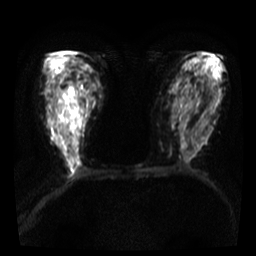
Breast MRI, one axial slice; position 19 of 36 along the scan axis; diffusion-weighted series; image 2 of 4 stored at this slice position (different b-values; order by instance number); 3 T; 256 × 256 image matrix, field of view 300 × 300 mm. Female patient.
Outlined on this slice (expert manual segmentation):
- tumour on diffusion-weighted imaging: bounding box <57,89,64,116> (left, top, right, bottom; pixels)